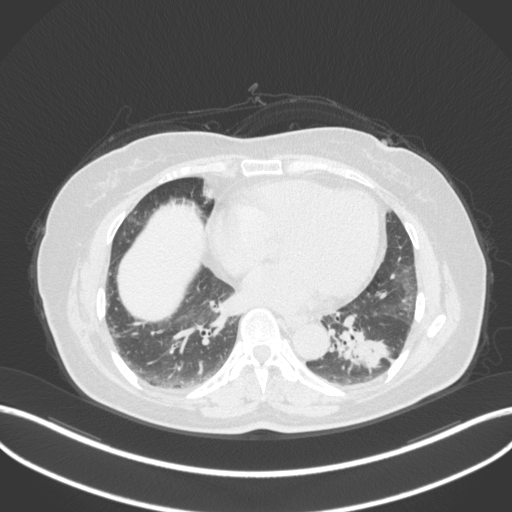
Chest CT, one axial slice; position 146 of 307 along the scan axis; reconstruction kernel B31f; lung window (W 1500 / L -600 HU); 1 mm slice thickness; 512 × 512 image matrix. Female patient, age 59 years. From the clinical record (not read from this slice): clinical TNM (as recorded): T2a N0 M0.
Outlined on this slice (rectangle marked by the reading radiologist):
- lung tumour (recorded histology: adenocarcinoma): bounding box (x1, y1, x2, y2) in pixels: (330, 314, 394, 373)